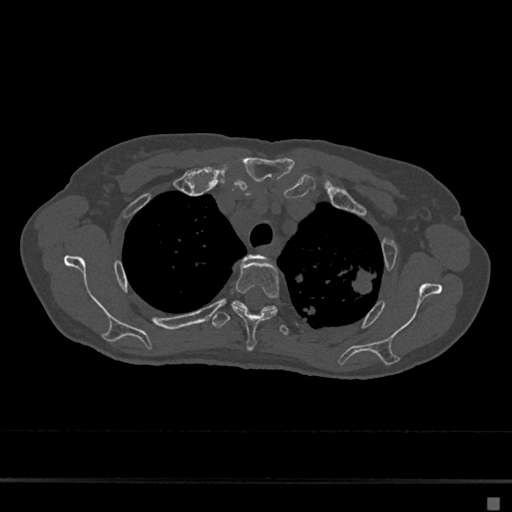
CT including the spine, one axial slice. Position 531 of 797 along the scan axis. Reconstruction kernel Br40s/3. 120 kVp. Bone window (W 1800 / L 400 HU). 0.5 mm slice thickness. 512 × 512 image matrix, field of view 360 × 360 mm. Patient: female, 68 years. Case-level facts recorded for this patient, not image findings: primary cancer: renal.
Annotated regions visible in this slice (semi-automatically segmented with operator editing):
- T2 vertebra: bounding box <232,255,266,307> (left, top, right, bottom; pixels)
- T3 vertebra: <232,259,279,351>
- T4 vertebra: <212,303,290,336>